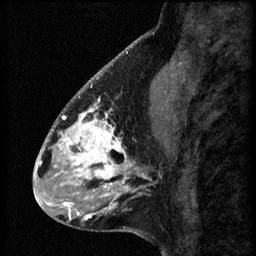
Breast MRI (dynamic contrast-enhanced), one sagittal slice. Slice 22 of 60 in the series (ordered by position). 3 images stored at this slice position (order not interpretable as contrast timing). 1.5 T. TE 4.2 ms, TR 8.2 ms. 2.2 mm slice thickness. 256 × 256 image matrix, field of view 180 × 180 mm. Female patient, age 41 years.
Annotated regions visible in this slice (semi-automatic segmentation, software-assisted and operator-edited):
- analysis volume of interest (the breast-tissue region the enhancement analysis was run in; not a lesion): box from (x=56, y=104) to (x=157, y=207) px
- tumour enhancement mask (voxels above the 70 % enhancement threshold inside the analysis volume of interest): (x=56, y=104)–(x=149, y=207)